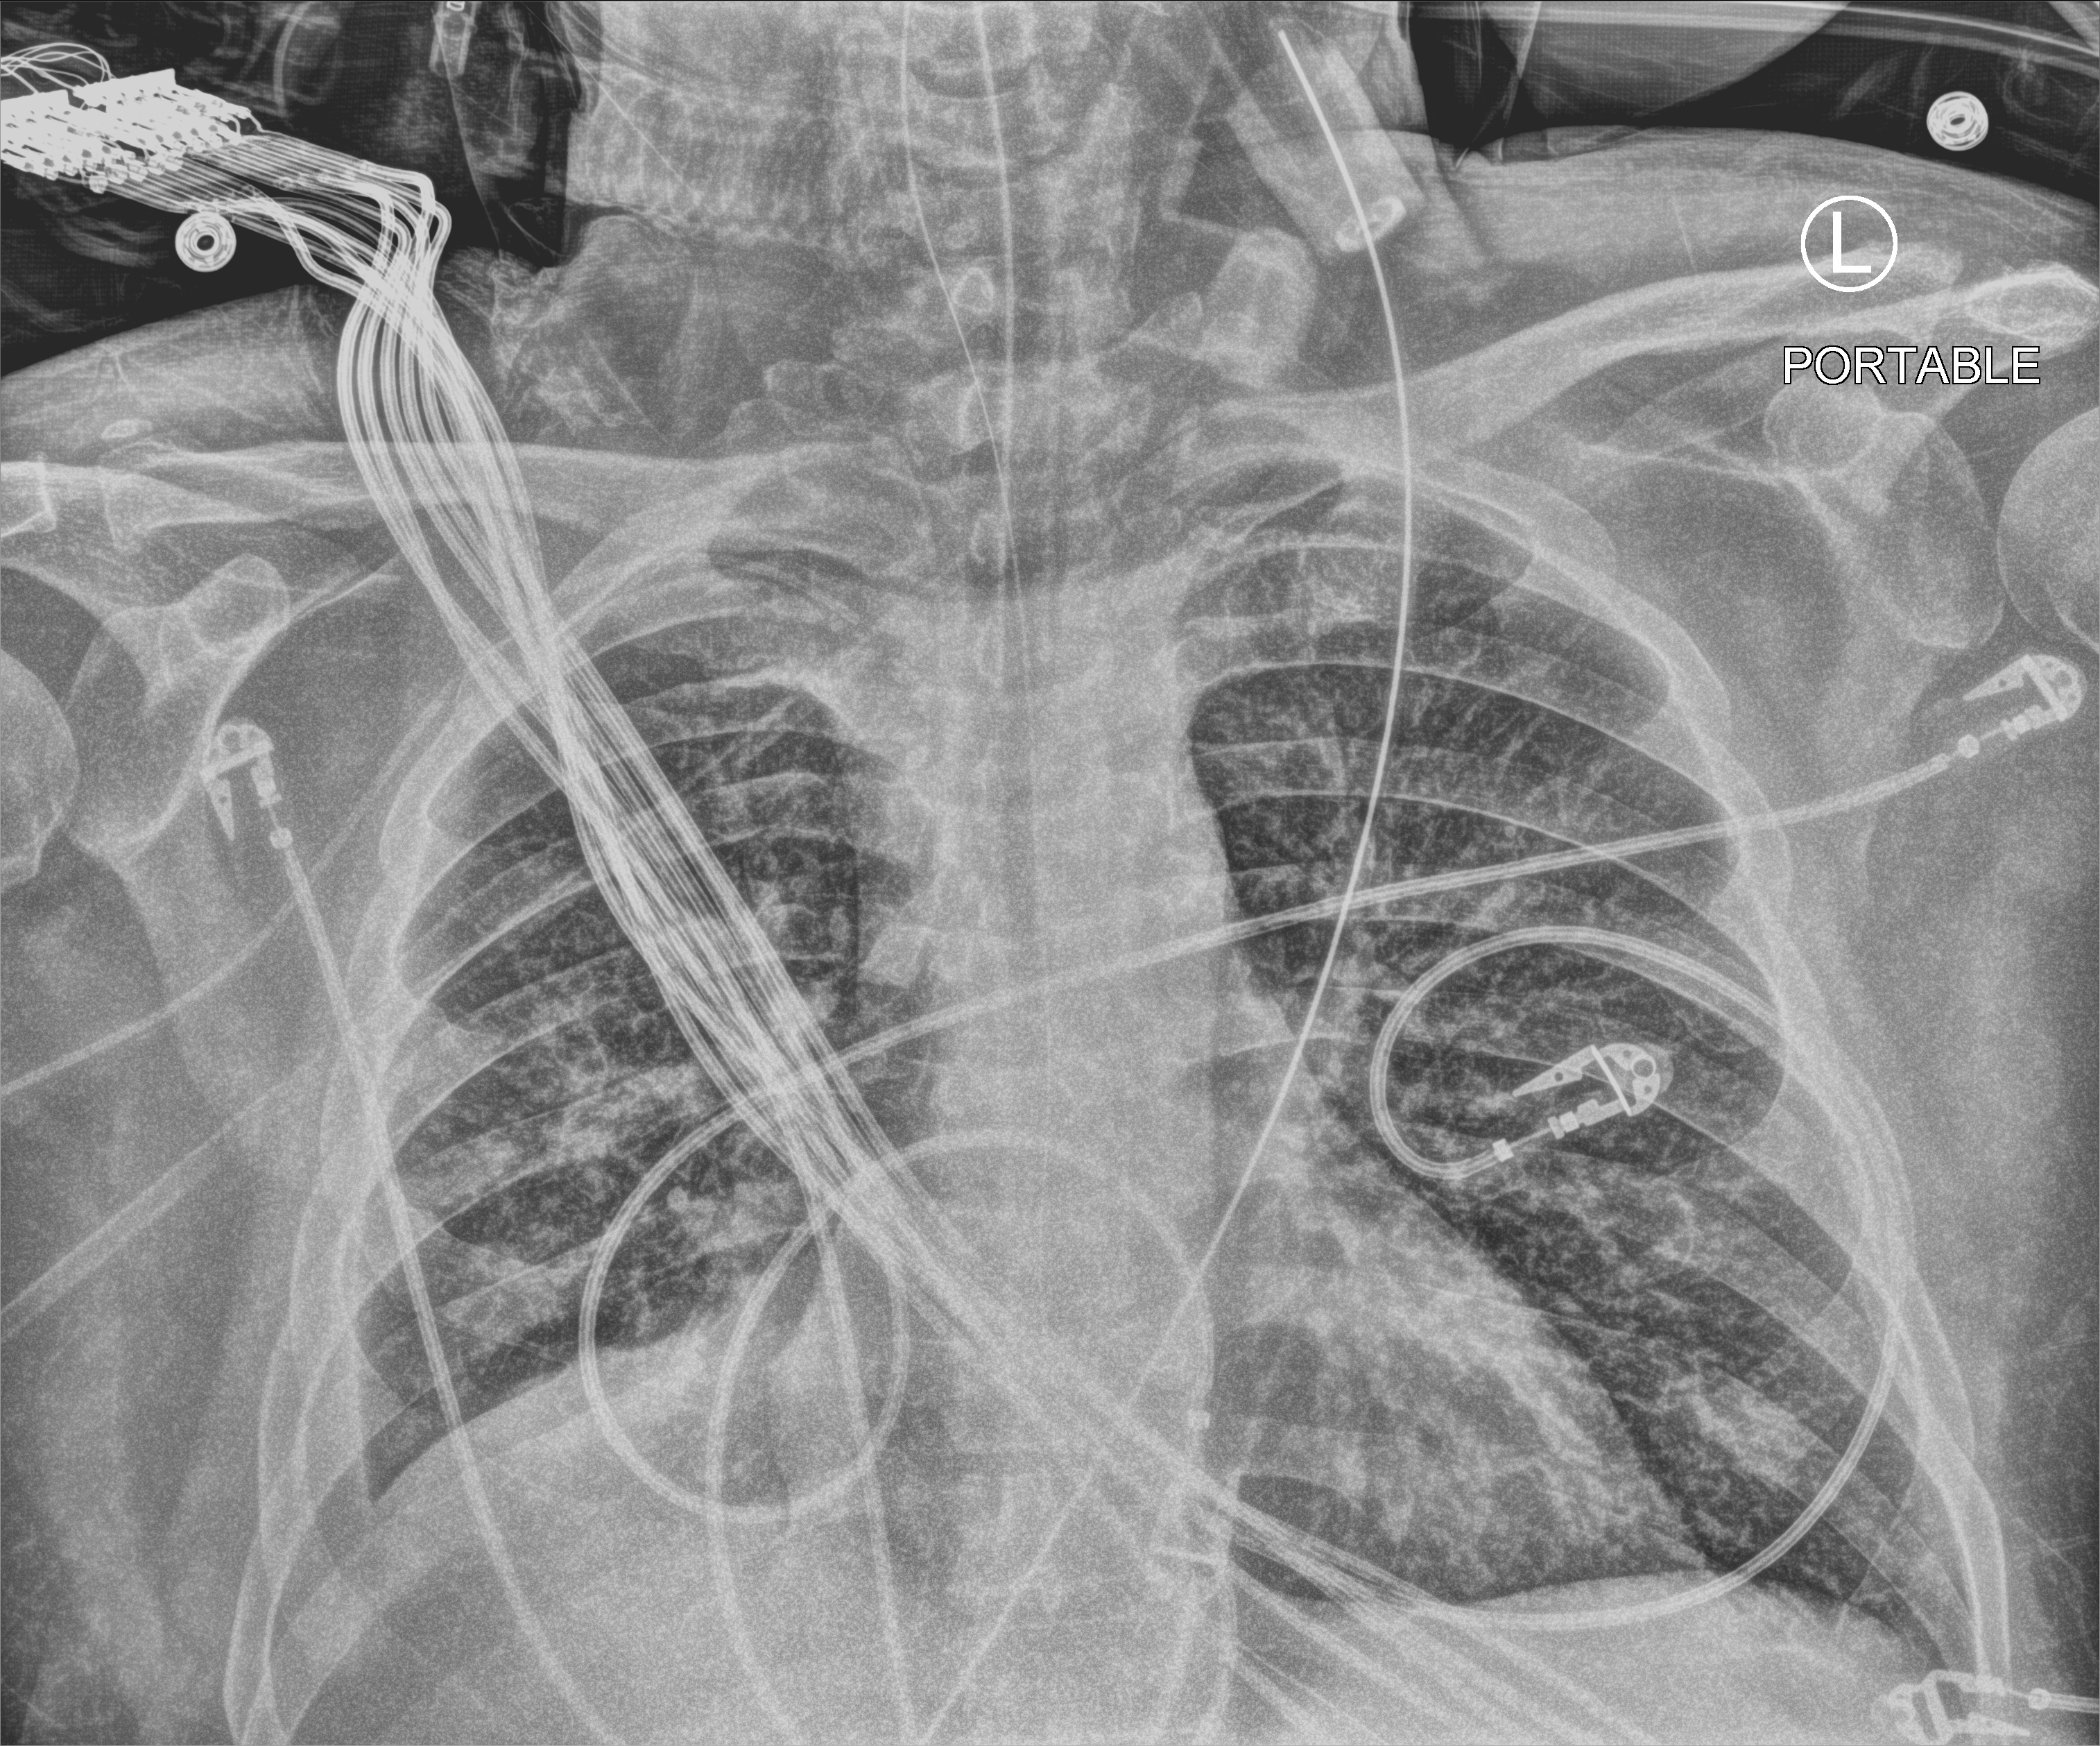
Chest X-ray (portable); anteroposterior (AP) projection. Patient hospitalised with COVID-19; male, aged 18–59 years.
Admission-level facts for this patient (not findings on this image; timing relative to this image not recorded): mechanically ventilated during this hospital stay: yes.